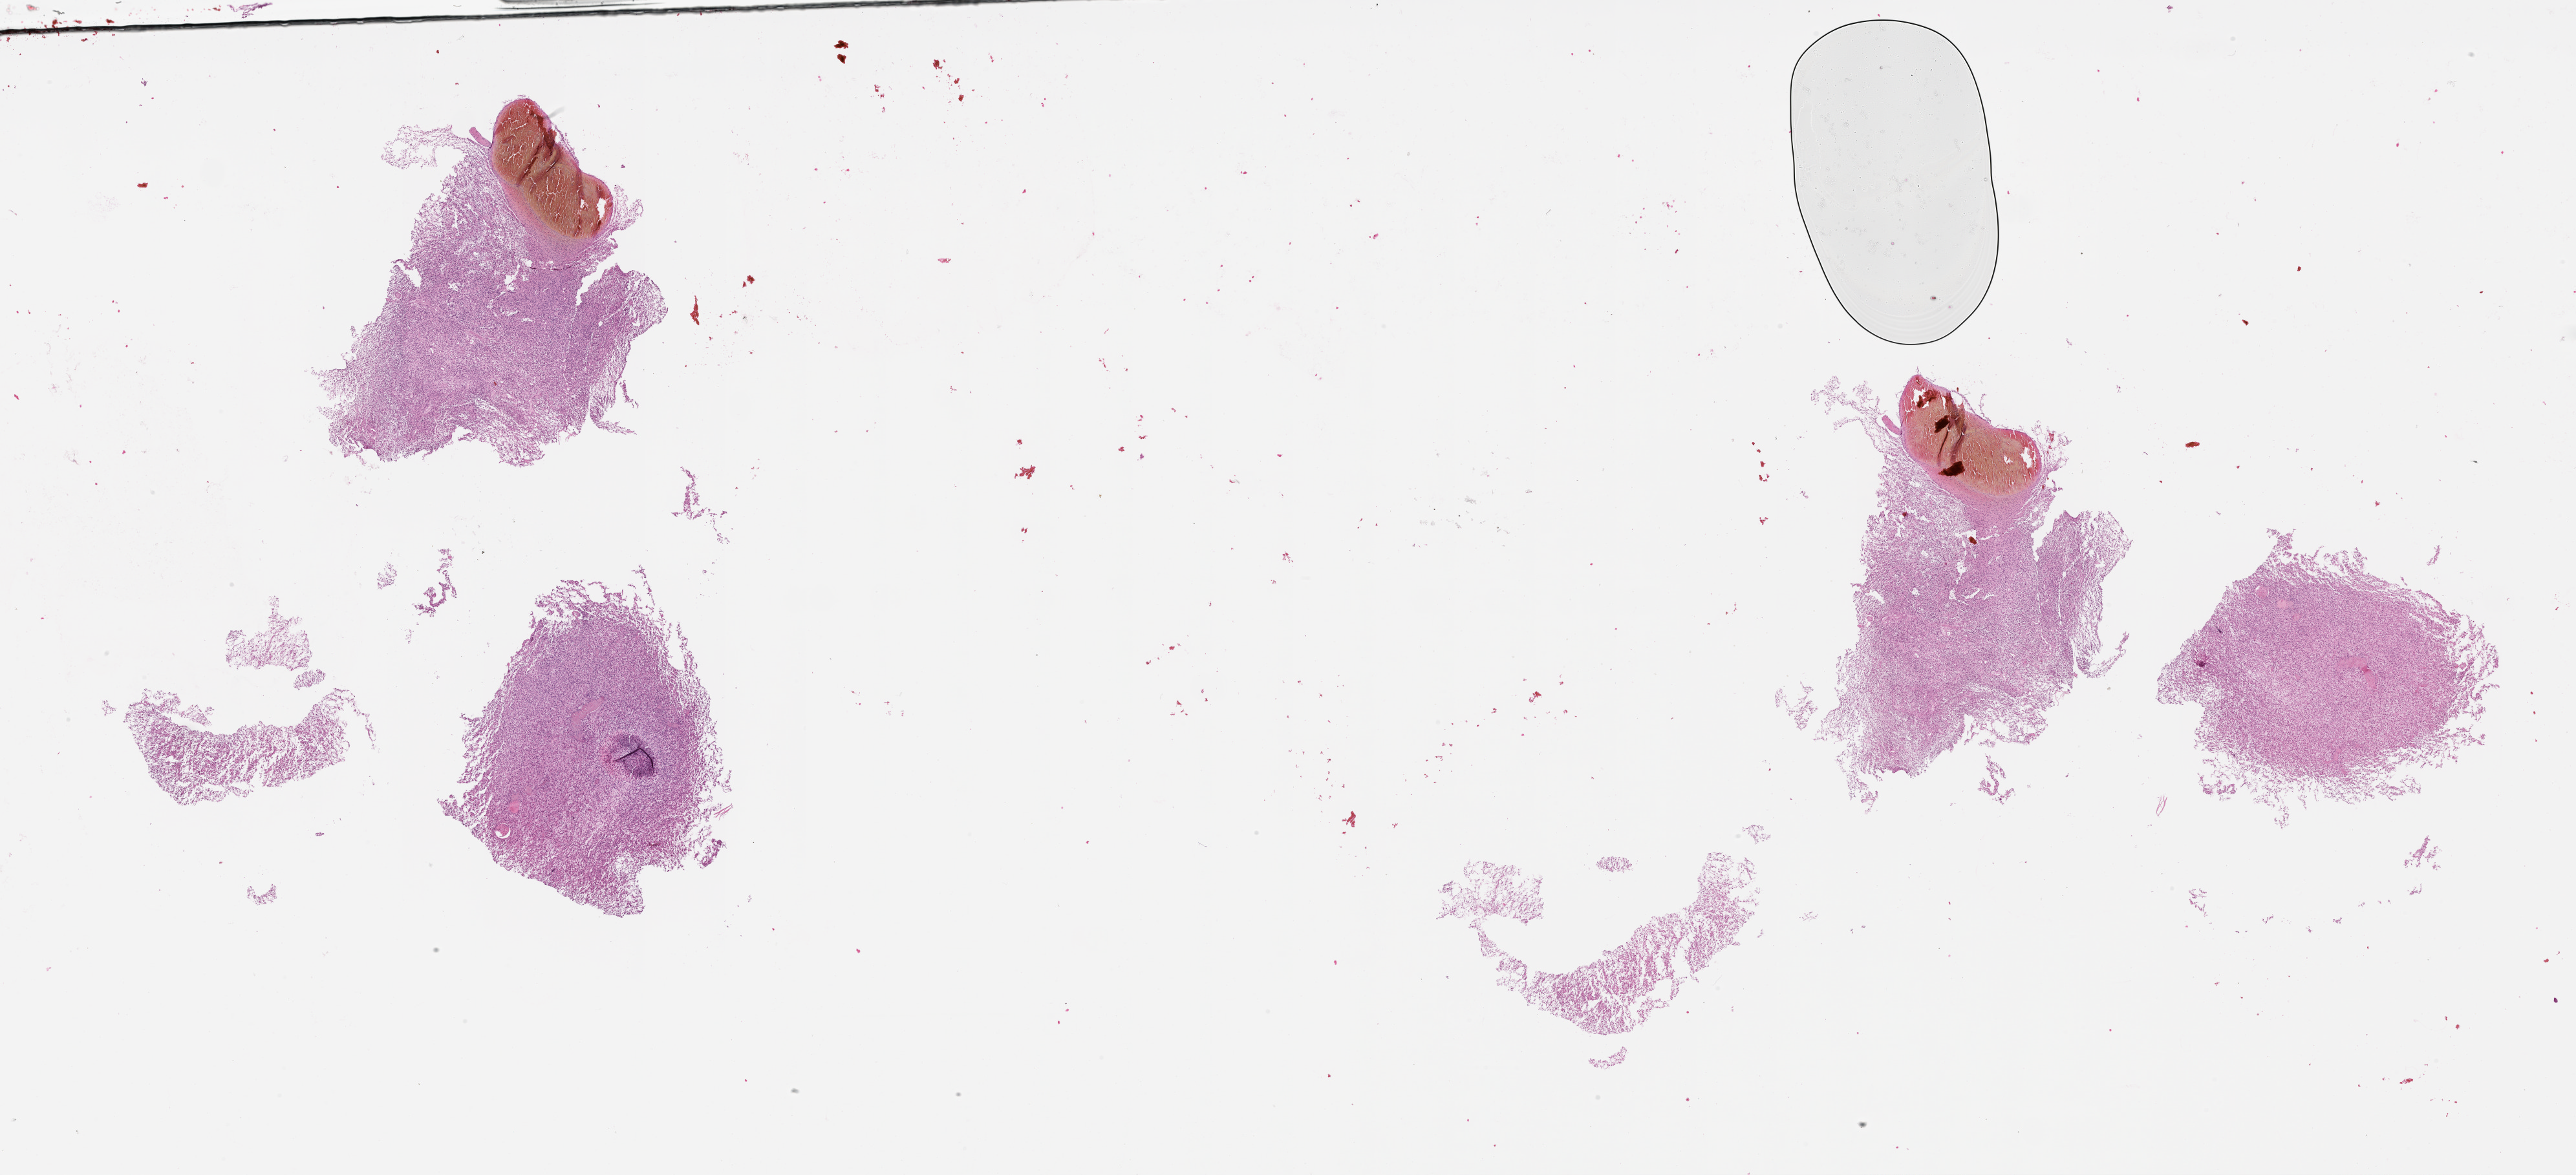
H&E whole-slide image, low-resolution overview of the scanned area, about 32.1 x 14.6 mm (acquisition: 20x scan); tumour tissue sample, sampled site: frontal lobe. 58-year-old male patient. Slide review estimates, as recorded: tumour nuclei 70%, necrosis 10%.
- diagnosis: Glioblastoma
- primary tumour site (as recorded): frontal lobe